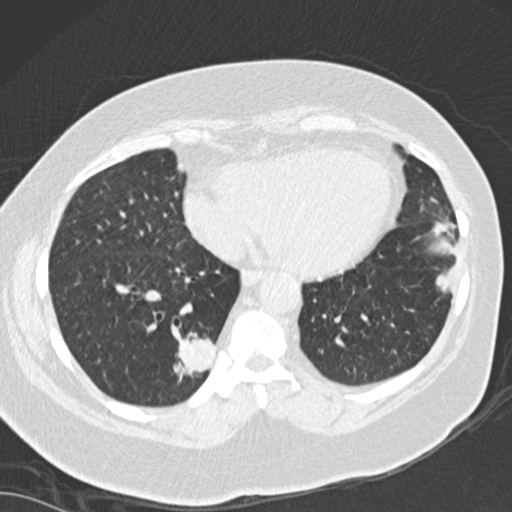
Low-dose screening chest CT, one axial slice; position 55 of 162 along the scan axis; lung window (W 1500 / L -600 HU); 2 mm slice thickness; 512 × 512 image matrix, field of view 328 × 328 mm.
Structures marked on this image (manually delineated by an expert):
- lesion 1 (tumor, lower lobe of right lung): bounding box (x1, y1, x2, y2) in pixels: (173, 332, 216, 383)